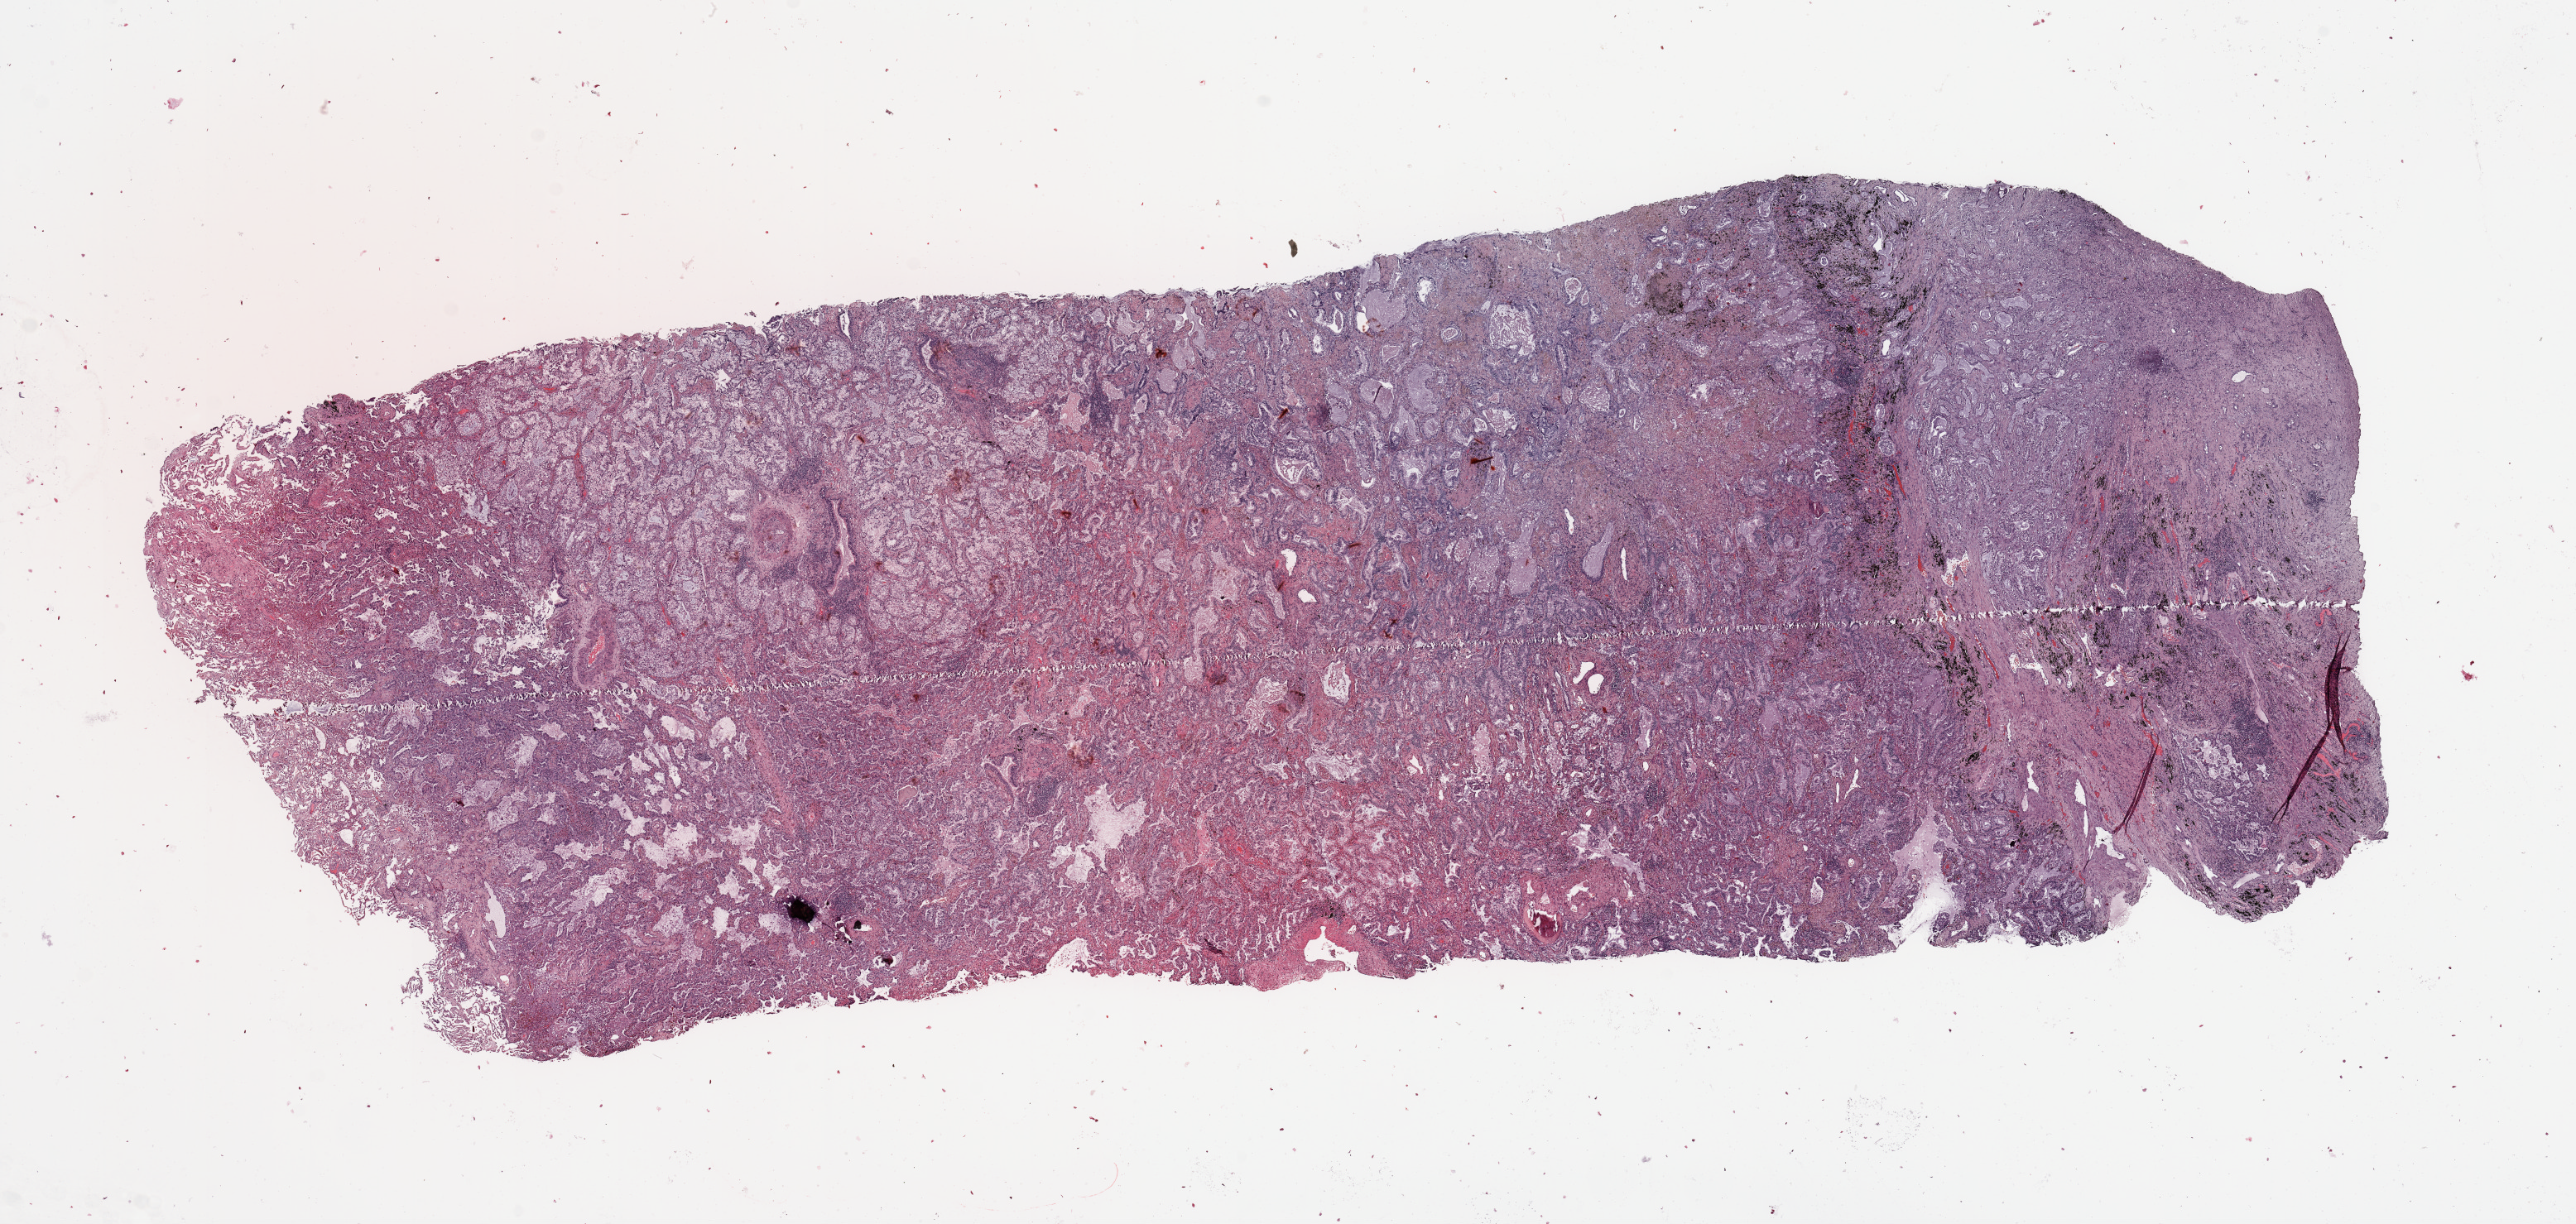
Digitized H&E tissue section (whole slide) — low-resolution overview of the scanned area, about 24.6 x 11.7 mm (acquisition: 20x scan). Tumour tissue sample, lung. Male, 64 y/o. Histologic grade: G2 (moderately differentiated).
Primary tumour site (as recorded): left lower lobe. Histologic diagnosis: Adenocarcinoma, NOS. AJCC pathologic stage: IIA.